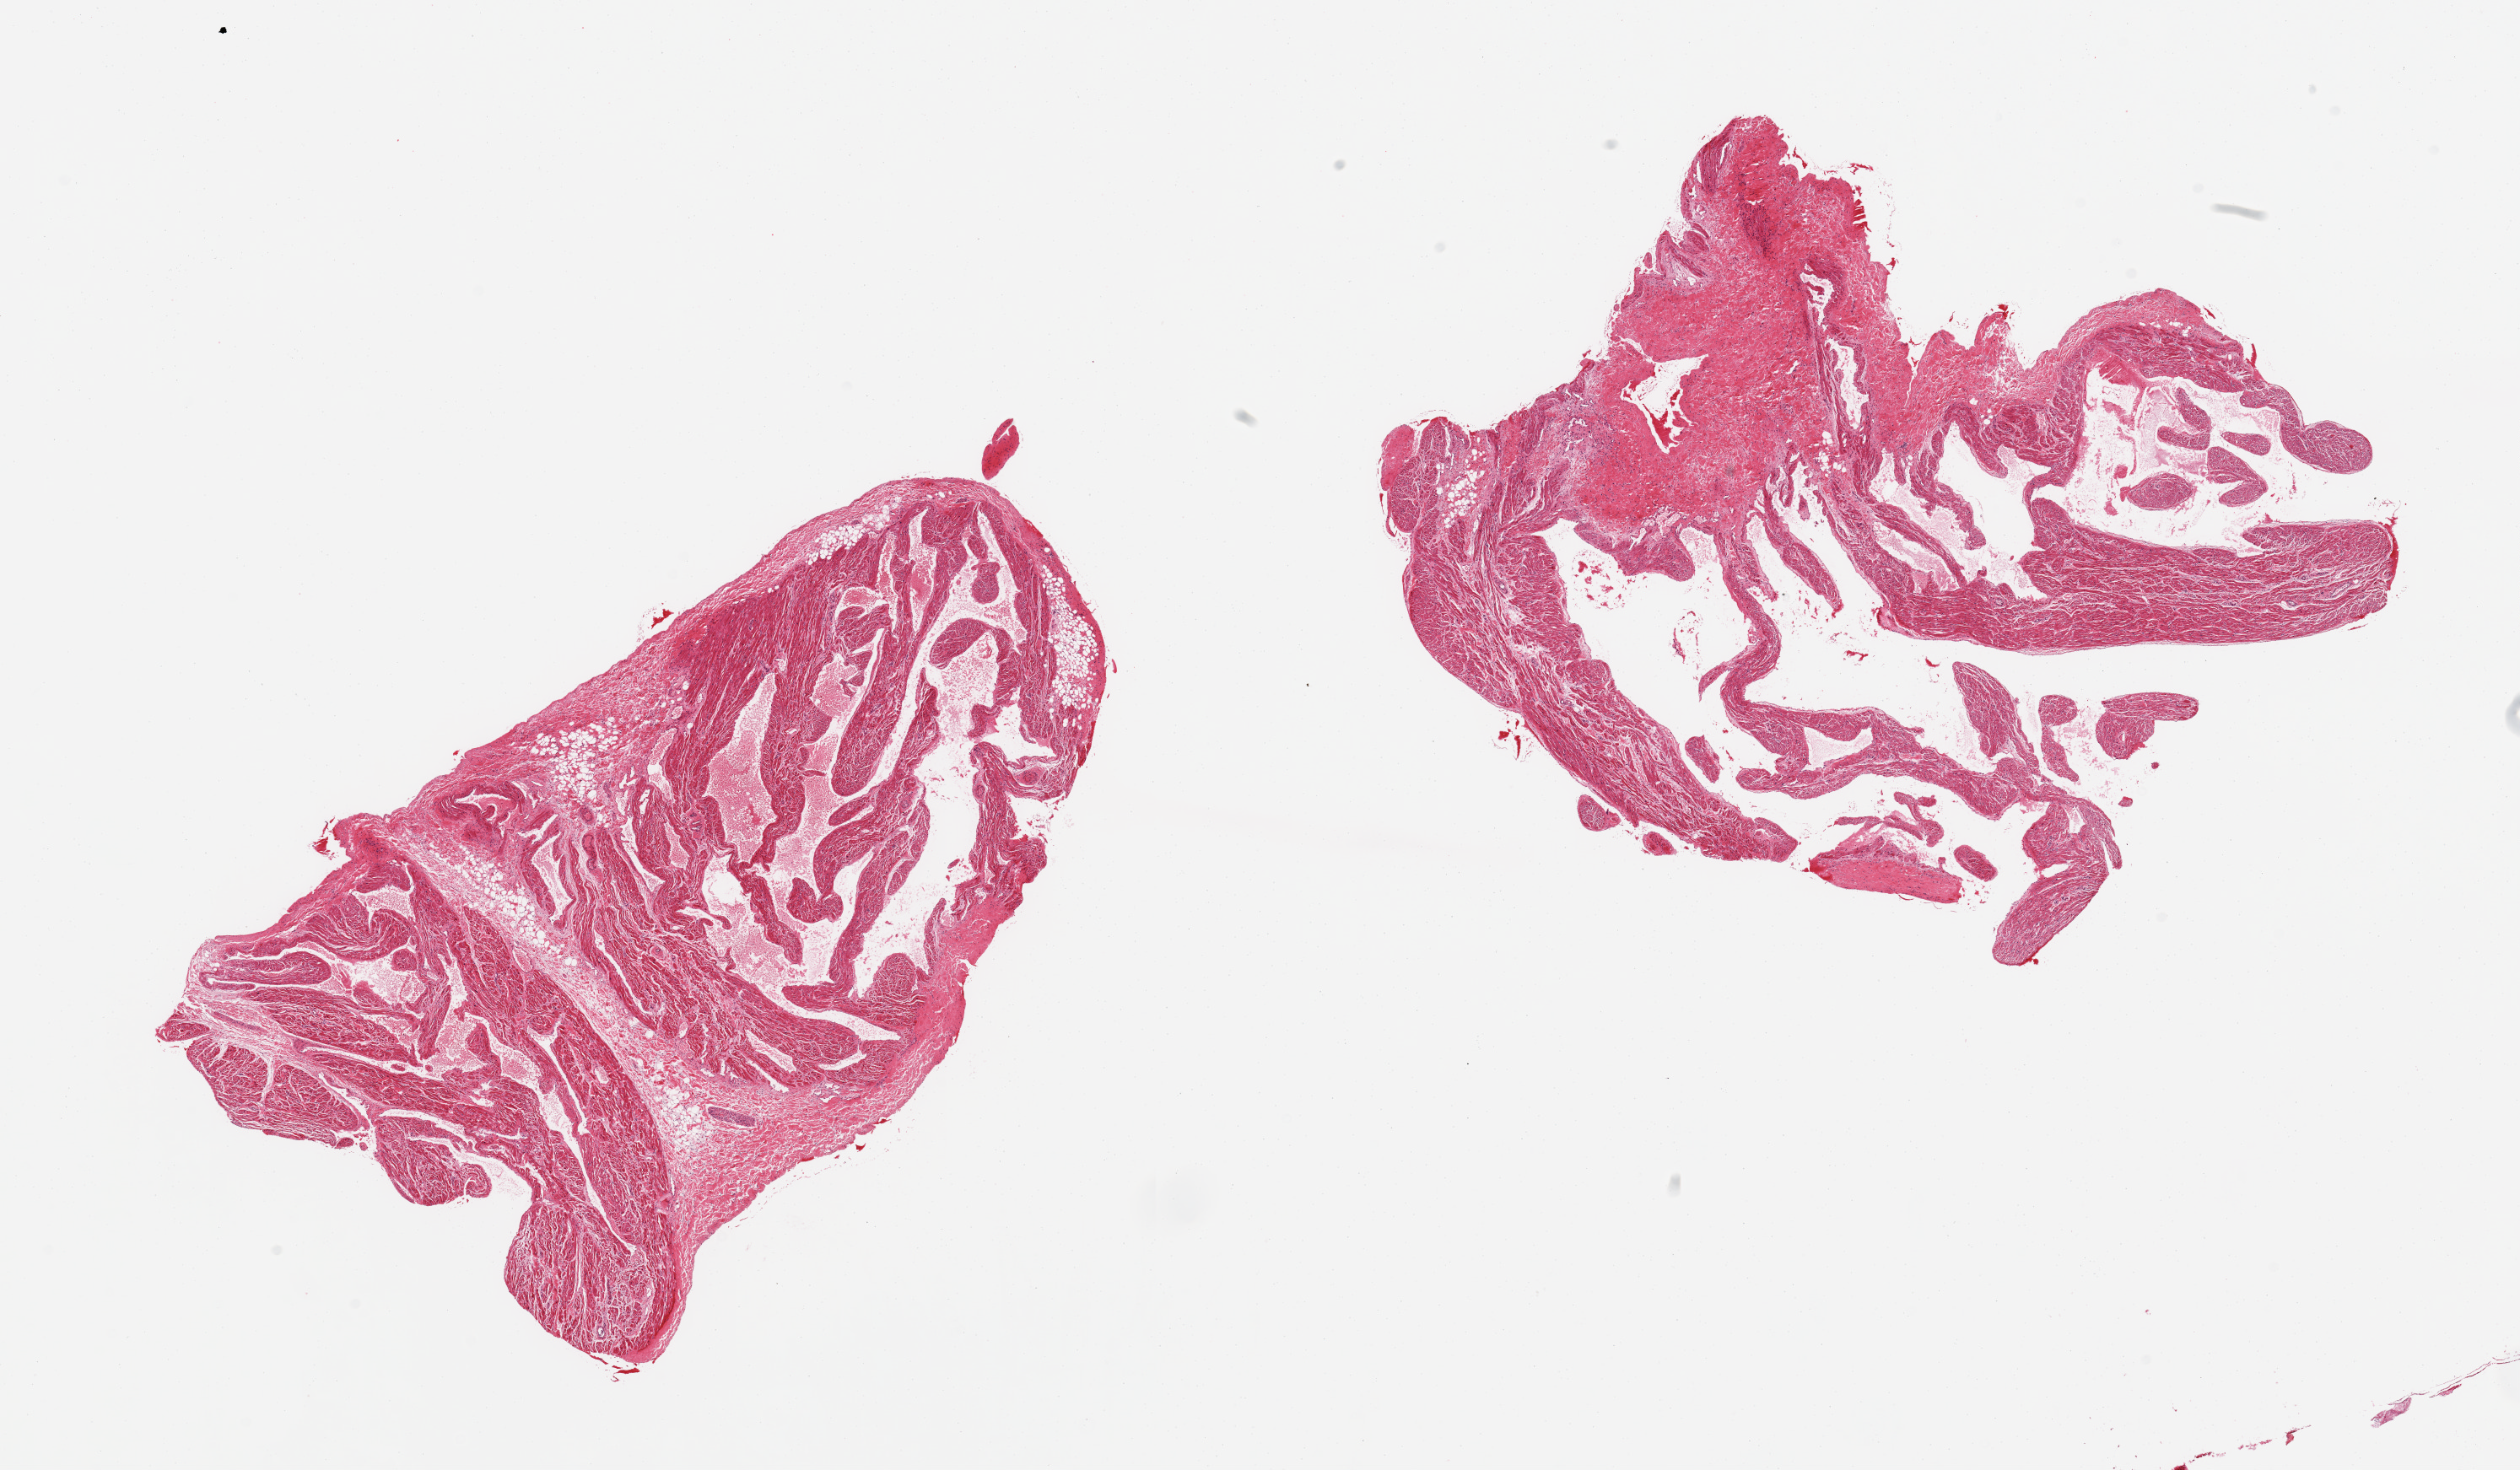
Digitized hematoxylin and eosin (H&E)-stained section, low-resolution overview of the scanned area, about 23.6 x 13.8 mm (acquisition: 20x scan), PAXgene-fixed paraffin-embedded (PFPE) section, section of auricular appendage (target tissue), donor tissue sample. Male donor.
Pathologist's review note for this sample: 2 pieces, no abnormalities.